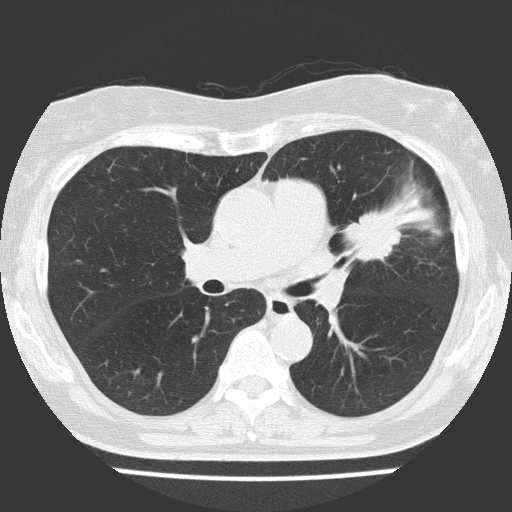
Axial slice from a low-dose chest CT screening exam. Baseline screening round. Lung window (W 1500 / L -600 HU). 2 mm slice thickness. 512 × 512 image matrix. Female participant, aged 70 years at enrolment. Current smoker at enrolment.
Expert-annotated lung lesion, box from (x=325, y=189) to (x=432, y=280) px. The screening reader recorded 2 non-calcified nodules or masses ≥4 mm on this exam; which of them this box marks is not recorded. Later outcome: lung cancer diagnosed 25 days after this screen — adenocarcinoma, NOS, left upper lobe, poorly differentiated (G3), stage IV (AJCC 6th edition), 30 mm at pathology.